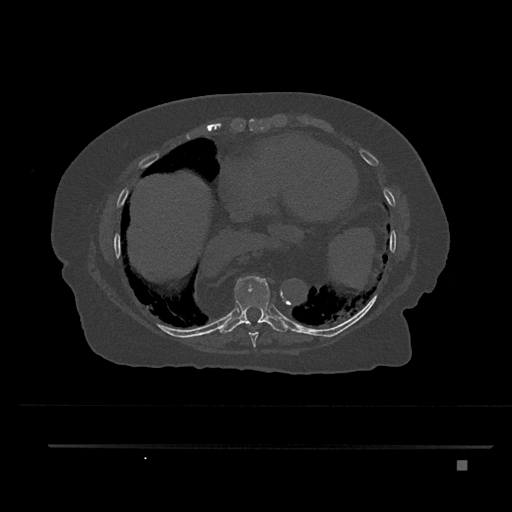
CT including the spine, one axial slice. Position 414 of 797 along the scan axis. Bone window (W 1800 / L 400 HU). 0.5 mm slice thickness. 512 × 512 image matrix, field of view 437 × 437 mm. Female patient, age 76 years. Case-level facts recorded for this patient, not image findings: primary cancer: lung; vertebrae with lytic lesions (as recorded): T11, L3.
Outlined on this slice (semi-automatically segmented with operator editing):
- T8 vertebra: box from (x=249, y=332) to (x=259, y=347) px
- T9 vertebra: (x=218, y=275)–(x=289, y=334)